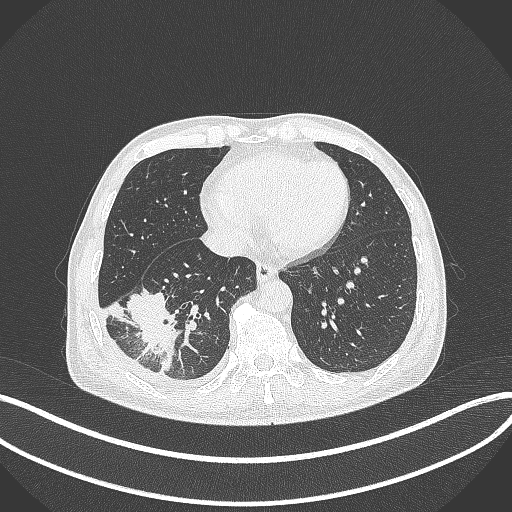
Chest CT, one axial slice. Slice 120 of 388 in the series (ordered by position). Reconstruction kernel B70f. Lung window (W 1500 / L -600 HU). 1 mm slice thickness. 512 × 512 image matrix, field of view 400 × 400 mm. Male patient, age 64 years. From the clinical record (not read from this slice): clinical TNM (as recorded): T3 N0 M0; histopathological grade: G2-3.
Structures marked on this image (rectangle marked by the reading radiologist):
- lung tumour (recorded histology: adenocarcinoma): bounding box <126,289,180,376> (left, top, right, bottom; pixels)